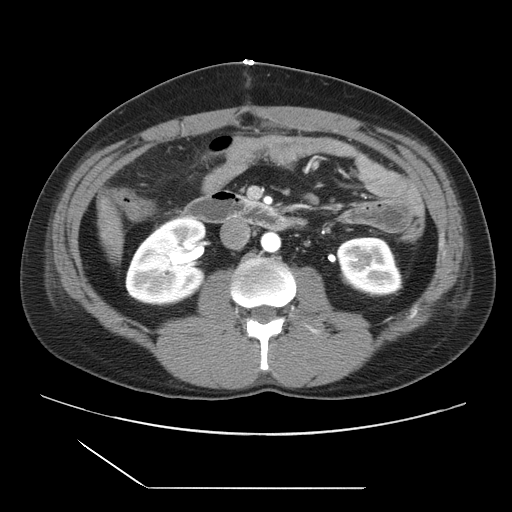
Contrast-enhanced abdominal CT, one axial slice; position 2 of 39 along the scan axis; intravenous contrast given; soft-tissue window (W 400 / L 40 HU); 5 mm slice thickness; 512 × 512 image matrix. Male patient, age 39 years. Case-level facts recorded for this patient, not image findings: diagnosis: colorectal cancer liver metastases, imaged before liver resection; multiple liver metastases: yes; largest metastasis: 1.3 cm.
Outlined on this slice (expert manual segmentation):
- liver: box from (x=102, y=205) to (x=118, y=252) px